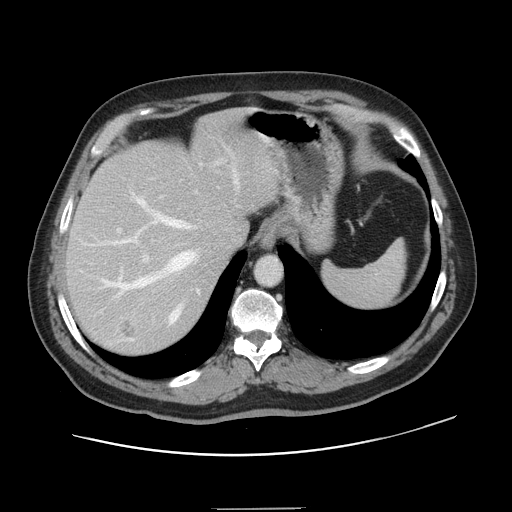
Contrast-enhanced abdominal CT, one axial slice. Position 111 of 143 along the scan axis. Intravenous contrast given. Soft-tissue window (W 400 / L 40 HU). 2.5 mm slice thickness. 512 × 512 image matrix, field of view 402 × 402 mm. Male patient, age 62 years. From the clinical record (not read from this slice): diagnosis: colorectal cancer liver metastases, imaged before liver resection; multiple liver metastases: yes; largest metastasis: 2.7 cm; disease in both lobes: no.
Outlined on this slice (manually delineated by an expert):
- hepatic veins: bounding box (x1, y1, x2, y2) in pixels: (101, 175, 239, 323)
- liver: (67, 114, 278, 355)
- planned liver remnant (the part of the liver to remain after resection): (67, 114, 278, 279)
- portal vein (with intrahepatic branches): (117, 160, 221, 340)
- liver metastasis: (121, 322, 137, 339)
- liver metastasis: (173, 163, 178, 171)